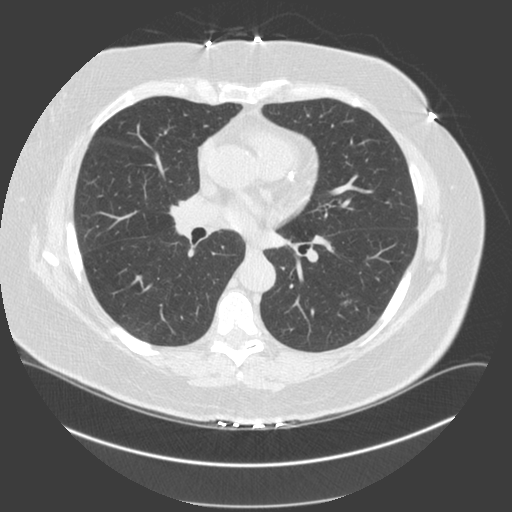
Low-dose screening chest CT, axial slice, second annual screen, lung window (W 1500 / L -600 HU), 2 mm slice thickness, standard (soft-tissue) reconstruction kernel (C), slice 77 of 179 in the series, 512 × 512 image matrix. Female participant, aged 66 years at enrolment. Current smoker at enrolment.
Expert-annotated lung lesion, bounding box <327,282,364,319> (left, top, right, bottom; pixels). Screening reader's record for this exam: no non-calcified nodule ≥4 mm recorded. Official screen result: negative screen, minor abnormalities not suspicious for lung cancer. Participant outcome: lung cancer diagnosed 495 days after this screen (after the third annual screen) — non-small cell carcinoma, left lower lobe, poorly differentiated (G3), stage IA (AJCC 6th edition), 20 mm at pathology.